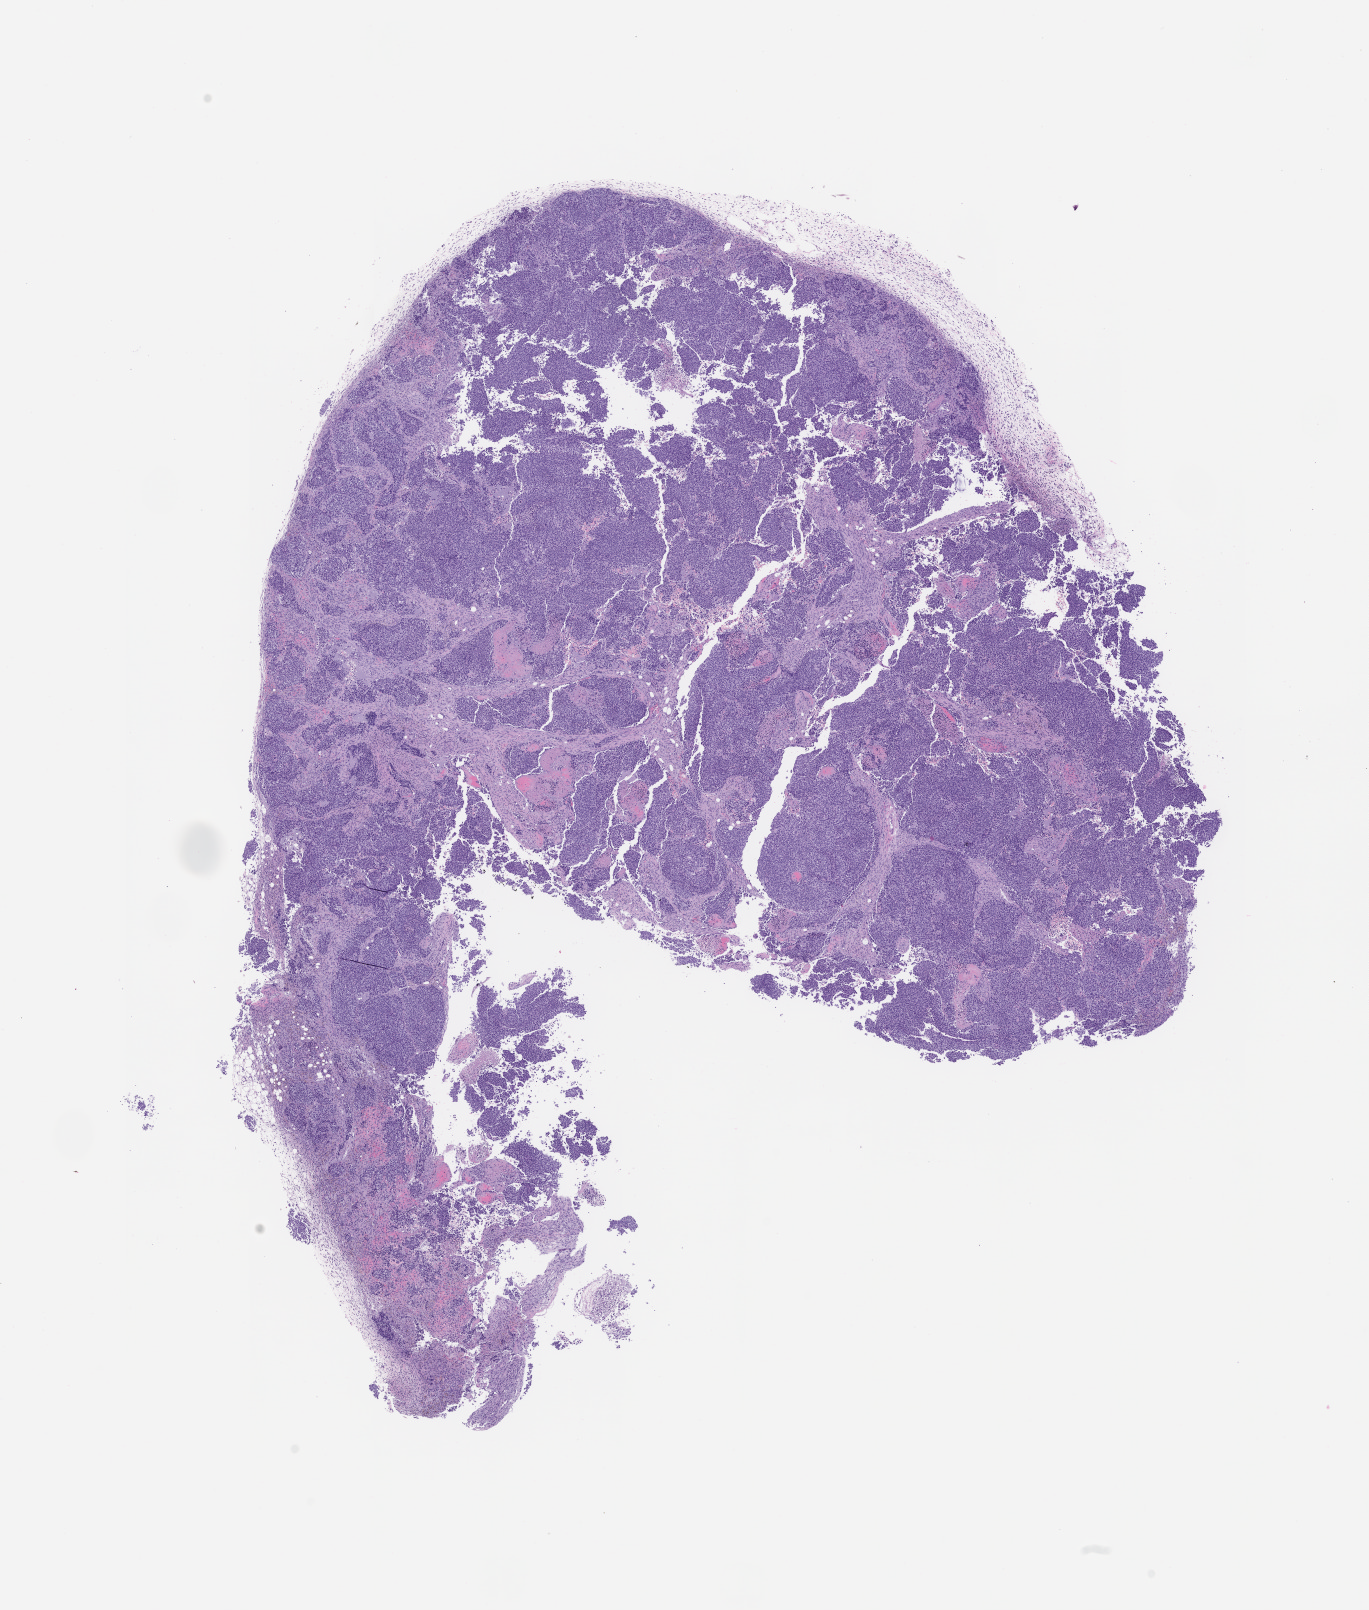
Haematoxylin and eosin whole-slide image of a patient-derived xenograft (PDX) tumor grown in a mouse — a low-resolution overview of the entire scanned area, about 11.0 x 12.9 mm; formalin-fixed paraffin-embedded section; originating tumor site category: lung.
Originating patient diagnosis: Lung Adenocarcinoma.